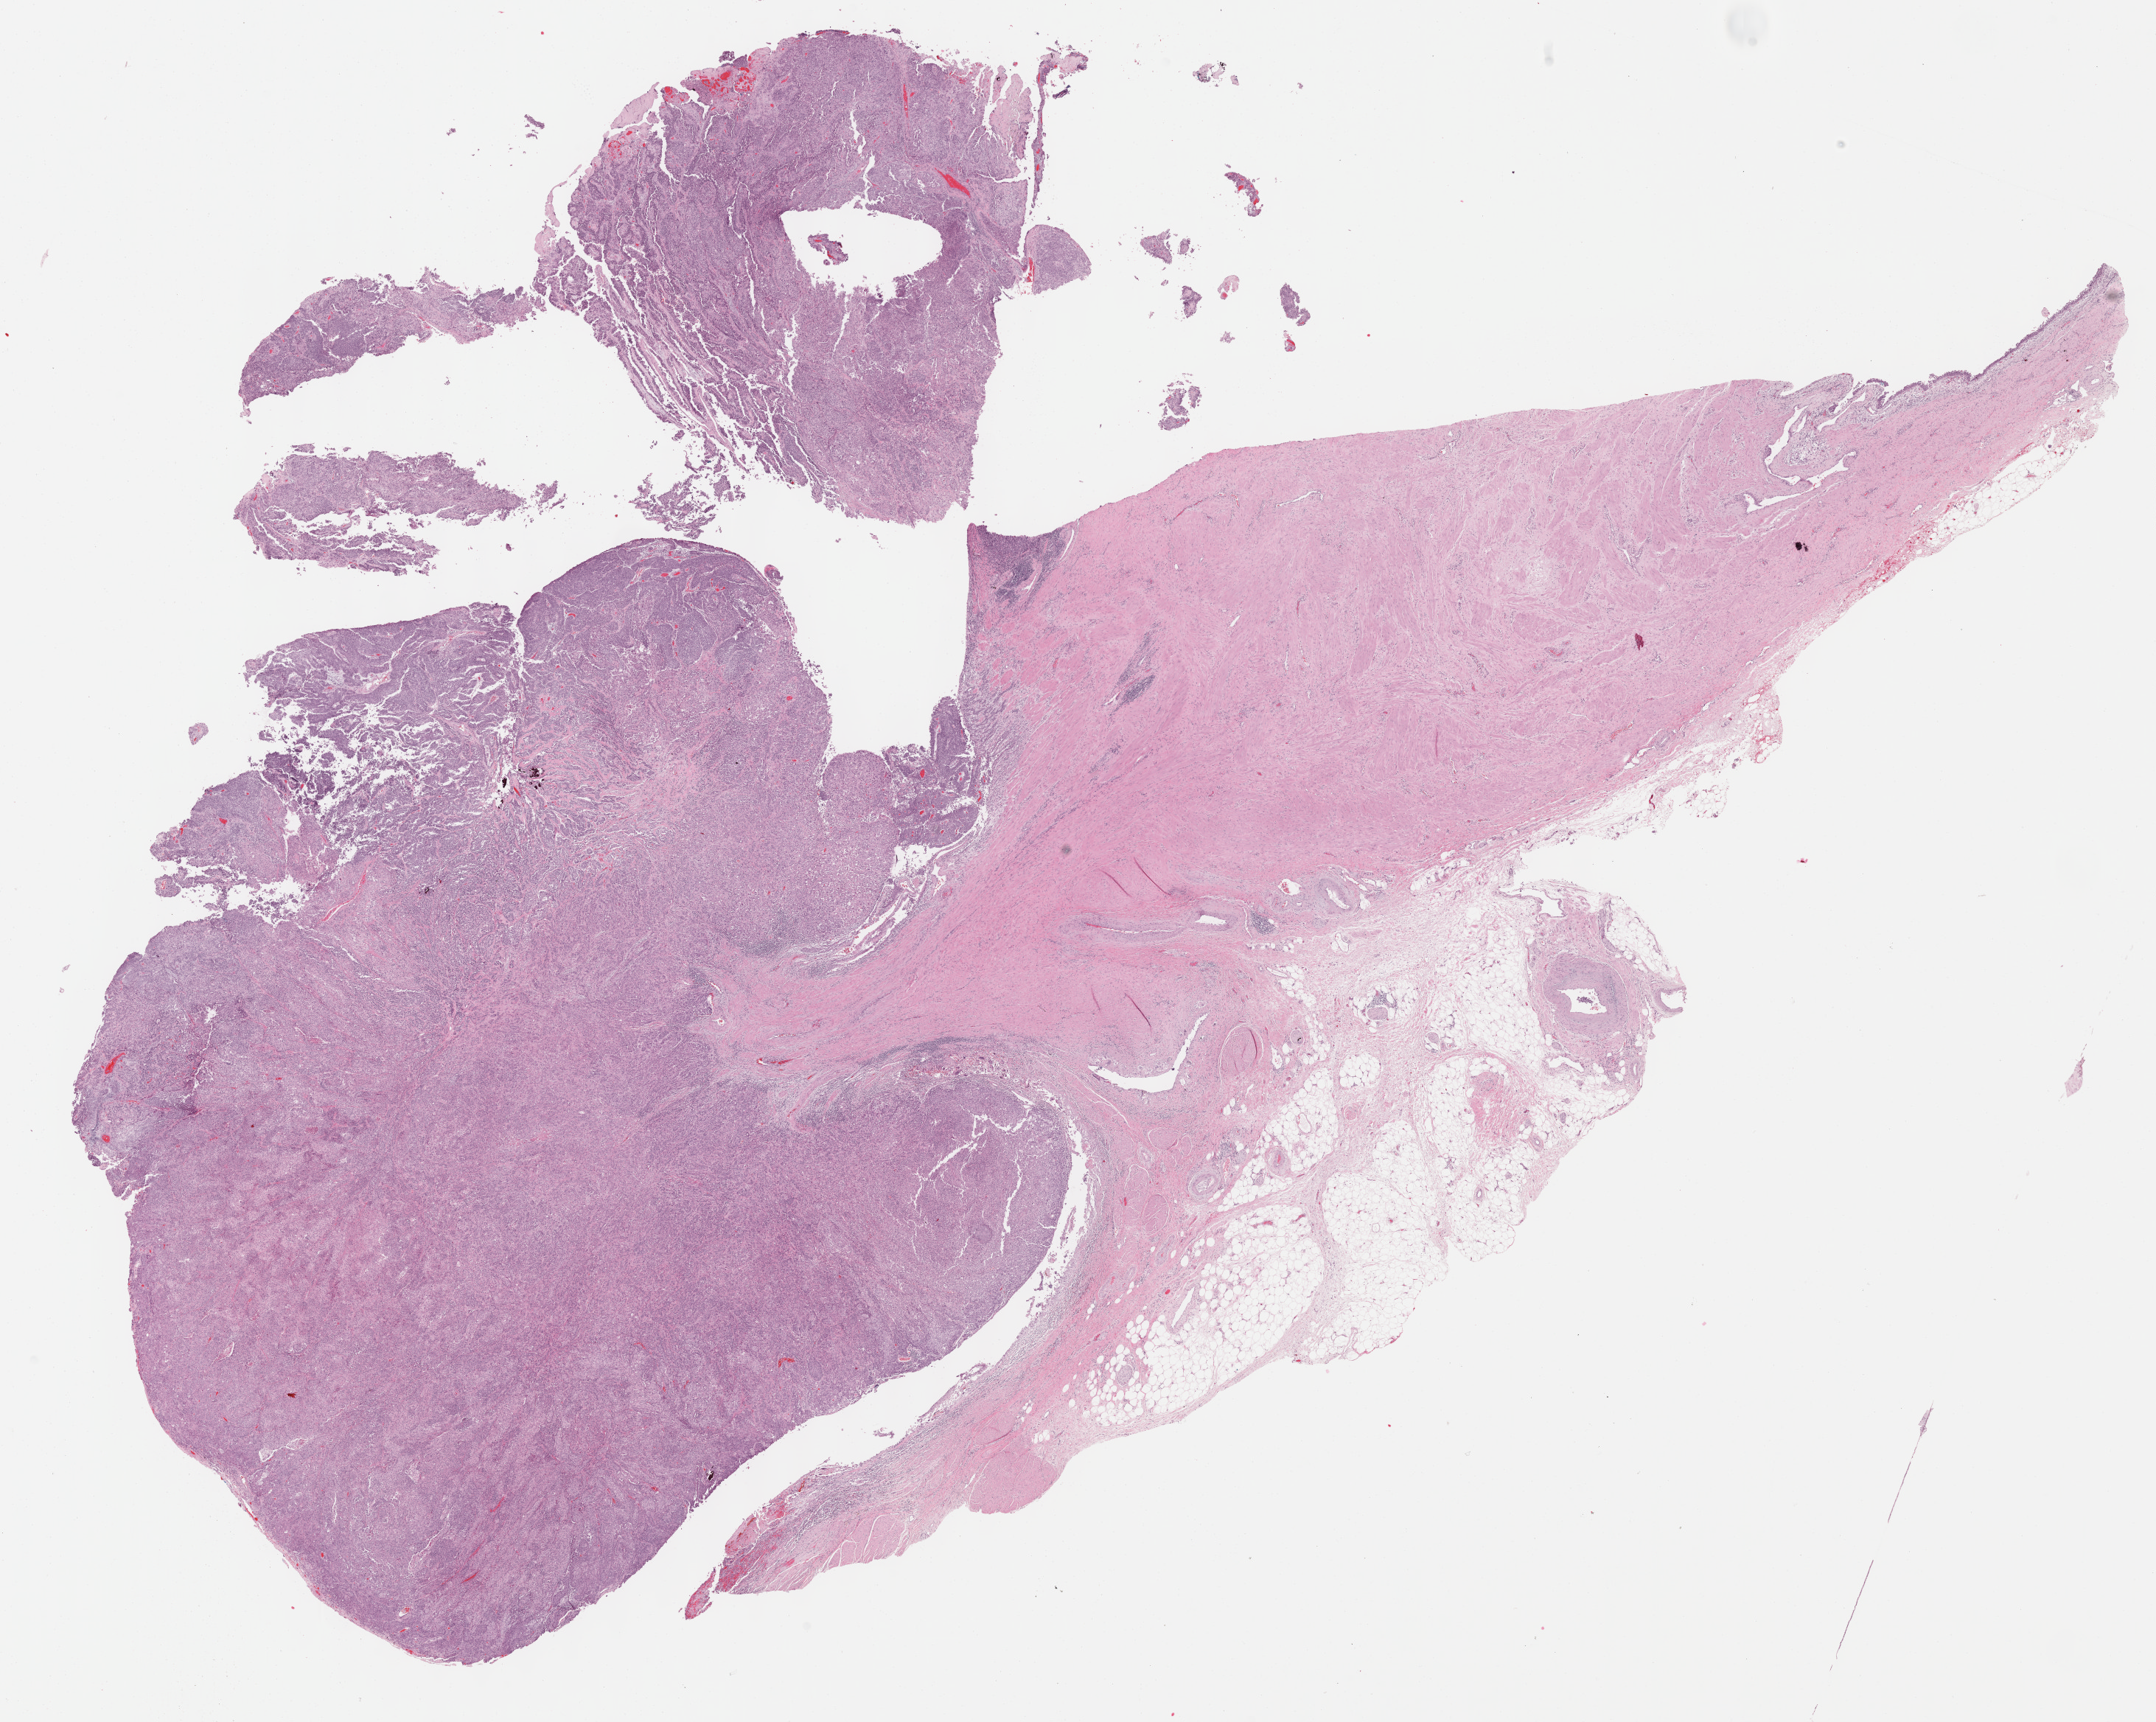
Digitized H&E tissue section (whole slide), a low-resolution overview of the entire scanned area, about 23.7 x 18.9 mm (acquisition: 40x scan), FFPE section, primary tumour sample from the bladder. Male patient; age at initial diagnosis 70 years.
Diagnosis: Transitional cell carcinoma (trigone of bladder).